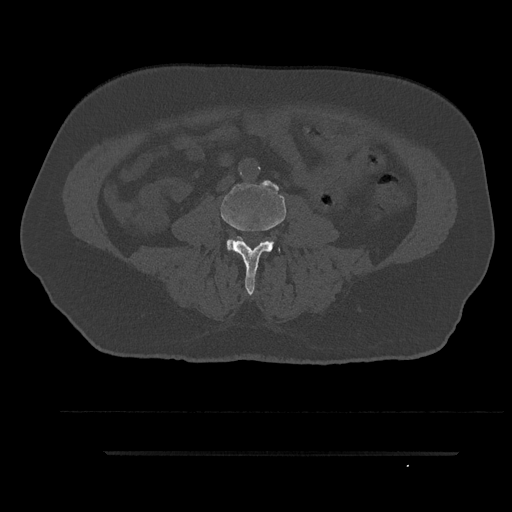
CT including the spine, one axial slice. Position 24 of 797 along the scan axis. 120 kVp. Bone window (W 1800 / L 400 HU). 0.5 mm slice thickness. 512 × 512 image matrix, field of view 432 × 432 mm. Male patient, age 63 years. From the clinical record (not read from this slice): primary cancer: renal.
Structures marked on this image (semi-automatic segmentation, software-assisted and operator-edited):
- L3 vertebra: bounding box <221,185,286,295> (left, top, right, bottom; pixels)
- L4 vertebra: <269,241,280,252>